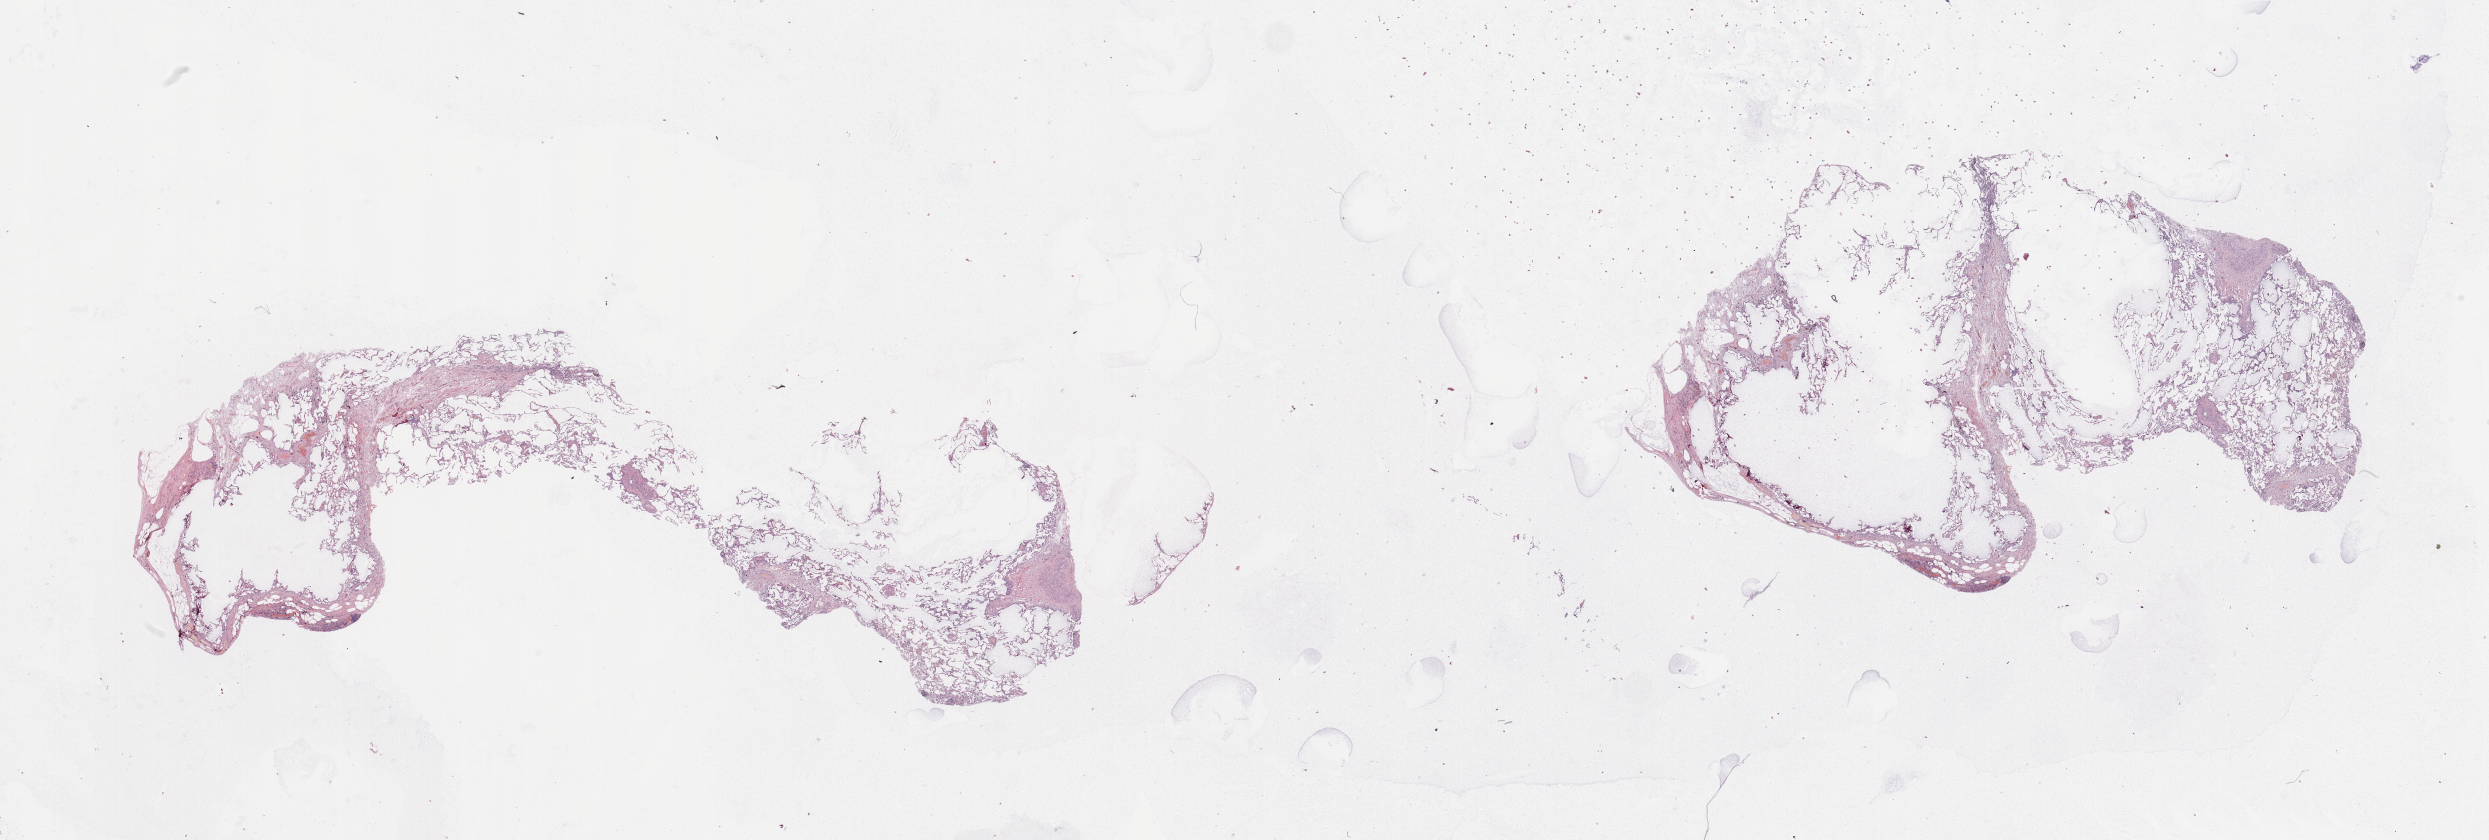
Whole-slide histology image, Hematoxylin and eosin (H&E) stained — shown as a low-resolution overview of the whole scanned area (about 39.4 x 13.3 mm, slide scanned at 20x), normal (non-tumour) tissue sample, lung. Male, 67 y/o.
This section: normal (non-tumour) tissue from the same patient. Patient diagnosis: Adenocarcinoma, NOS.